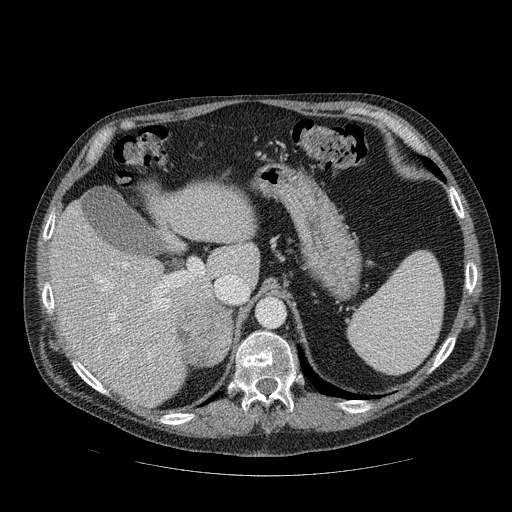
Contrast-enhanced abdominal CT, one axial slice. Slice 67 of 111 in the series (ordered by position). 120 kVp. Soft-tissue window (W 400 / L 40 HU). 2.5 mm slice thickness. 512 × 512 image matrix, field of view 420 × 420 mm. Patient: male, 56 years. From the clinical record (not read from this slice): diagnosis: adrenocortical carcinoma; tumour side: right adrenal; tumour size at pathology: 9 cm; Ki-67 index: 48 %.
Outlined on this slice (semi-automatic segmentation, software-assisted and operator-edited):
- mass: box from (x=176, y=303) to (x=232, y=365) px